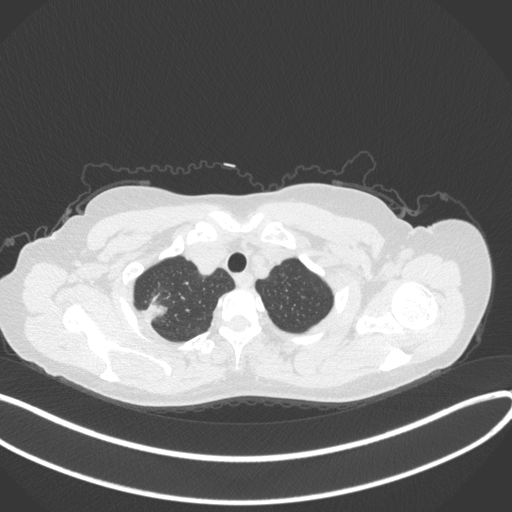
Chest CT, one axial slice. Slice 324 of 342 in the series (ordered by position). Reconstruction kernel B31f. 120 kVp. Lung window (W 1500 / L -600 HU). 1 mm slice thickness. 512 × 512 image matrix, field of view 400 × 400 mm. Patient: female, 50 years. Case-level facts recorded for this patient, not image findings: clinical TNM (as recorded): T1c N0 M0; histopathological grade: G2-3.
Annotated regions visible in this slice (bounding box drawn by a radiologist):
- lung tumour (recorded histology: adenocarcinoma): bounding box <144,300,166,321> (left, top, right, bottom; pixels)